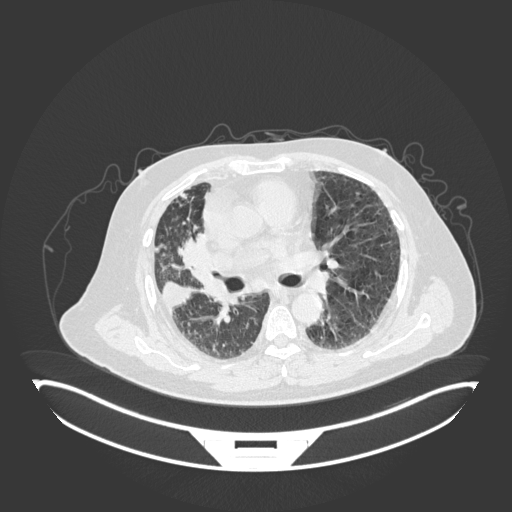
Chest CT, one axial slice. Reconstruction kernel B30f. Lung window (W 1500 / L -600 HU). 512 × 512 image matrix, field of view 500 × 500 mm. Patient: male, 69 years. From the clinical record (not read from this slice): clinical TNM (as recorded): T4 N3 M1.
Annotated regions visible in this slice (bounding box drawn by a radiologist):
- lung tumour (recorded histology: adenocarcinoma): bounding box (x1, y1, x2, y2) in pixels: (173, 226, 214, 271)